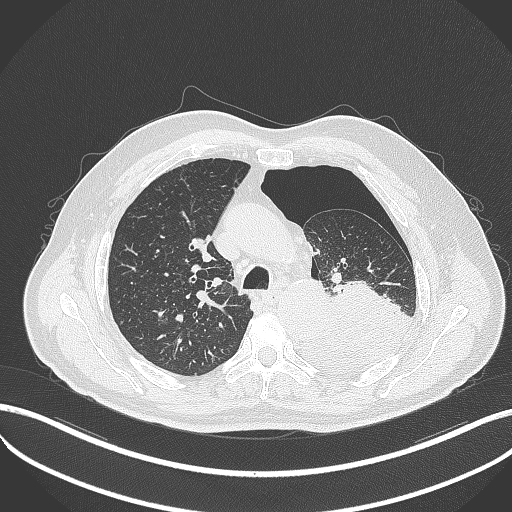
Chest CT, one axial slice; reconstruction kernel B70f; 120 kVp; lung window (W 1500 / L -600 HU); 512 × 512 image matrix, field of view 400 × 400 mm. Male patient, age 76 years. From the clinical record (not read from this slice): clinical TNM (as recorded): T3 N0 M1b.
Annotated regions visible in this slice (bounding box drawn by a radiologist):
- lung tumour (recorded histology: adenocarcinoma): bounding box [x1, y1, x2, y2] px = [297, 278, 416, 371]